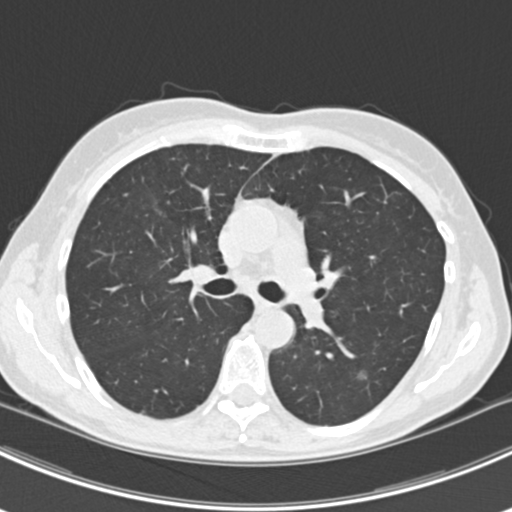
Chest CT (low-dose screening protocol), one axial image; first (baseline) screen; lung window (W 1500 / L -600 HU); 2 mm slice thickness; slice 72 of 224 in the series; 512 × 512 image matrix. Female participant, aged 63 years at enrolment. Current smoker at enrolment.
Lesion marked by an expert reader, box from (x=341, y=362) to (x=378, y=392) px. The screening reader recorded 10 non-calcified nodules or masses ≥4 mm on this exam (right lower lobe, right lower lobe, left lower lobe, left lower lobe, right middle lobe, right lower lobe, left lower lobe, left upper lobe, right upper lobe, left upper lobe); which of them this box marks is not recorded.